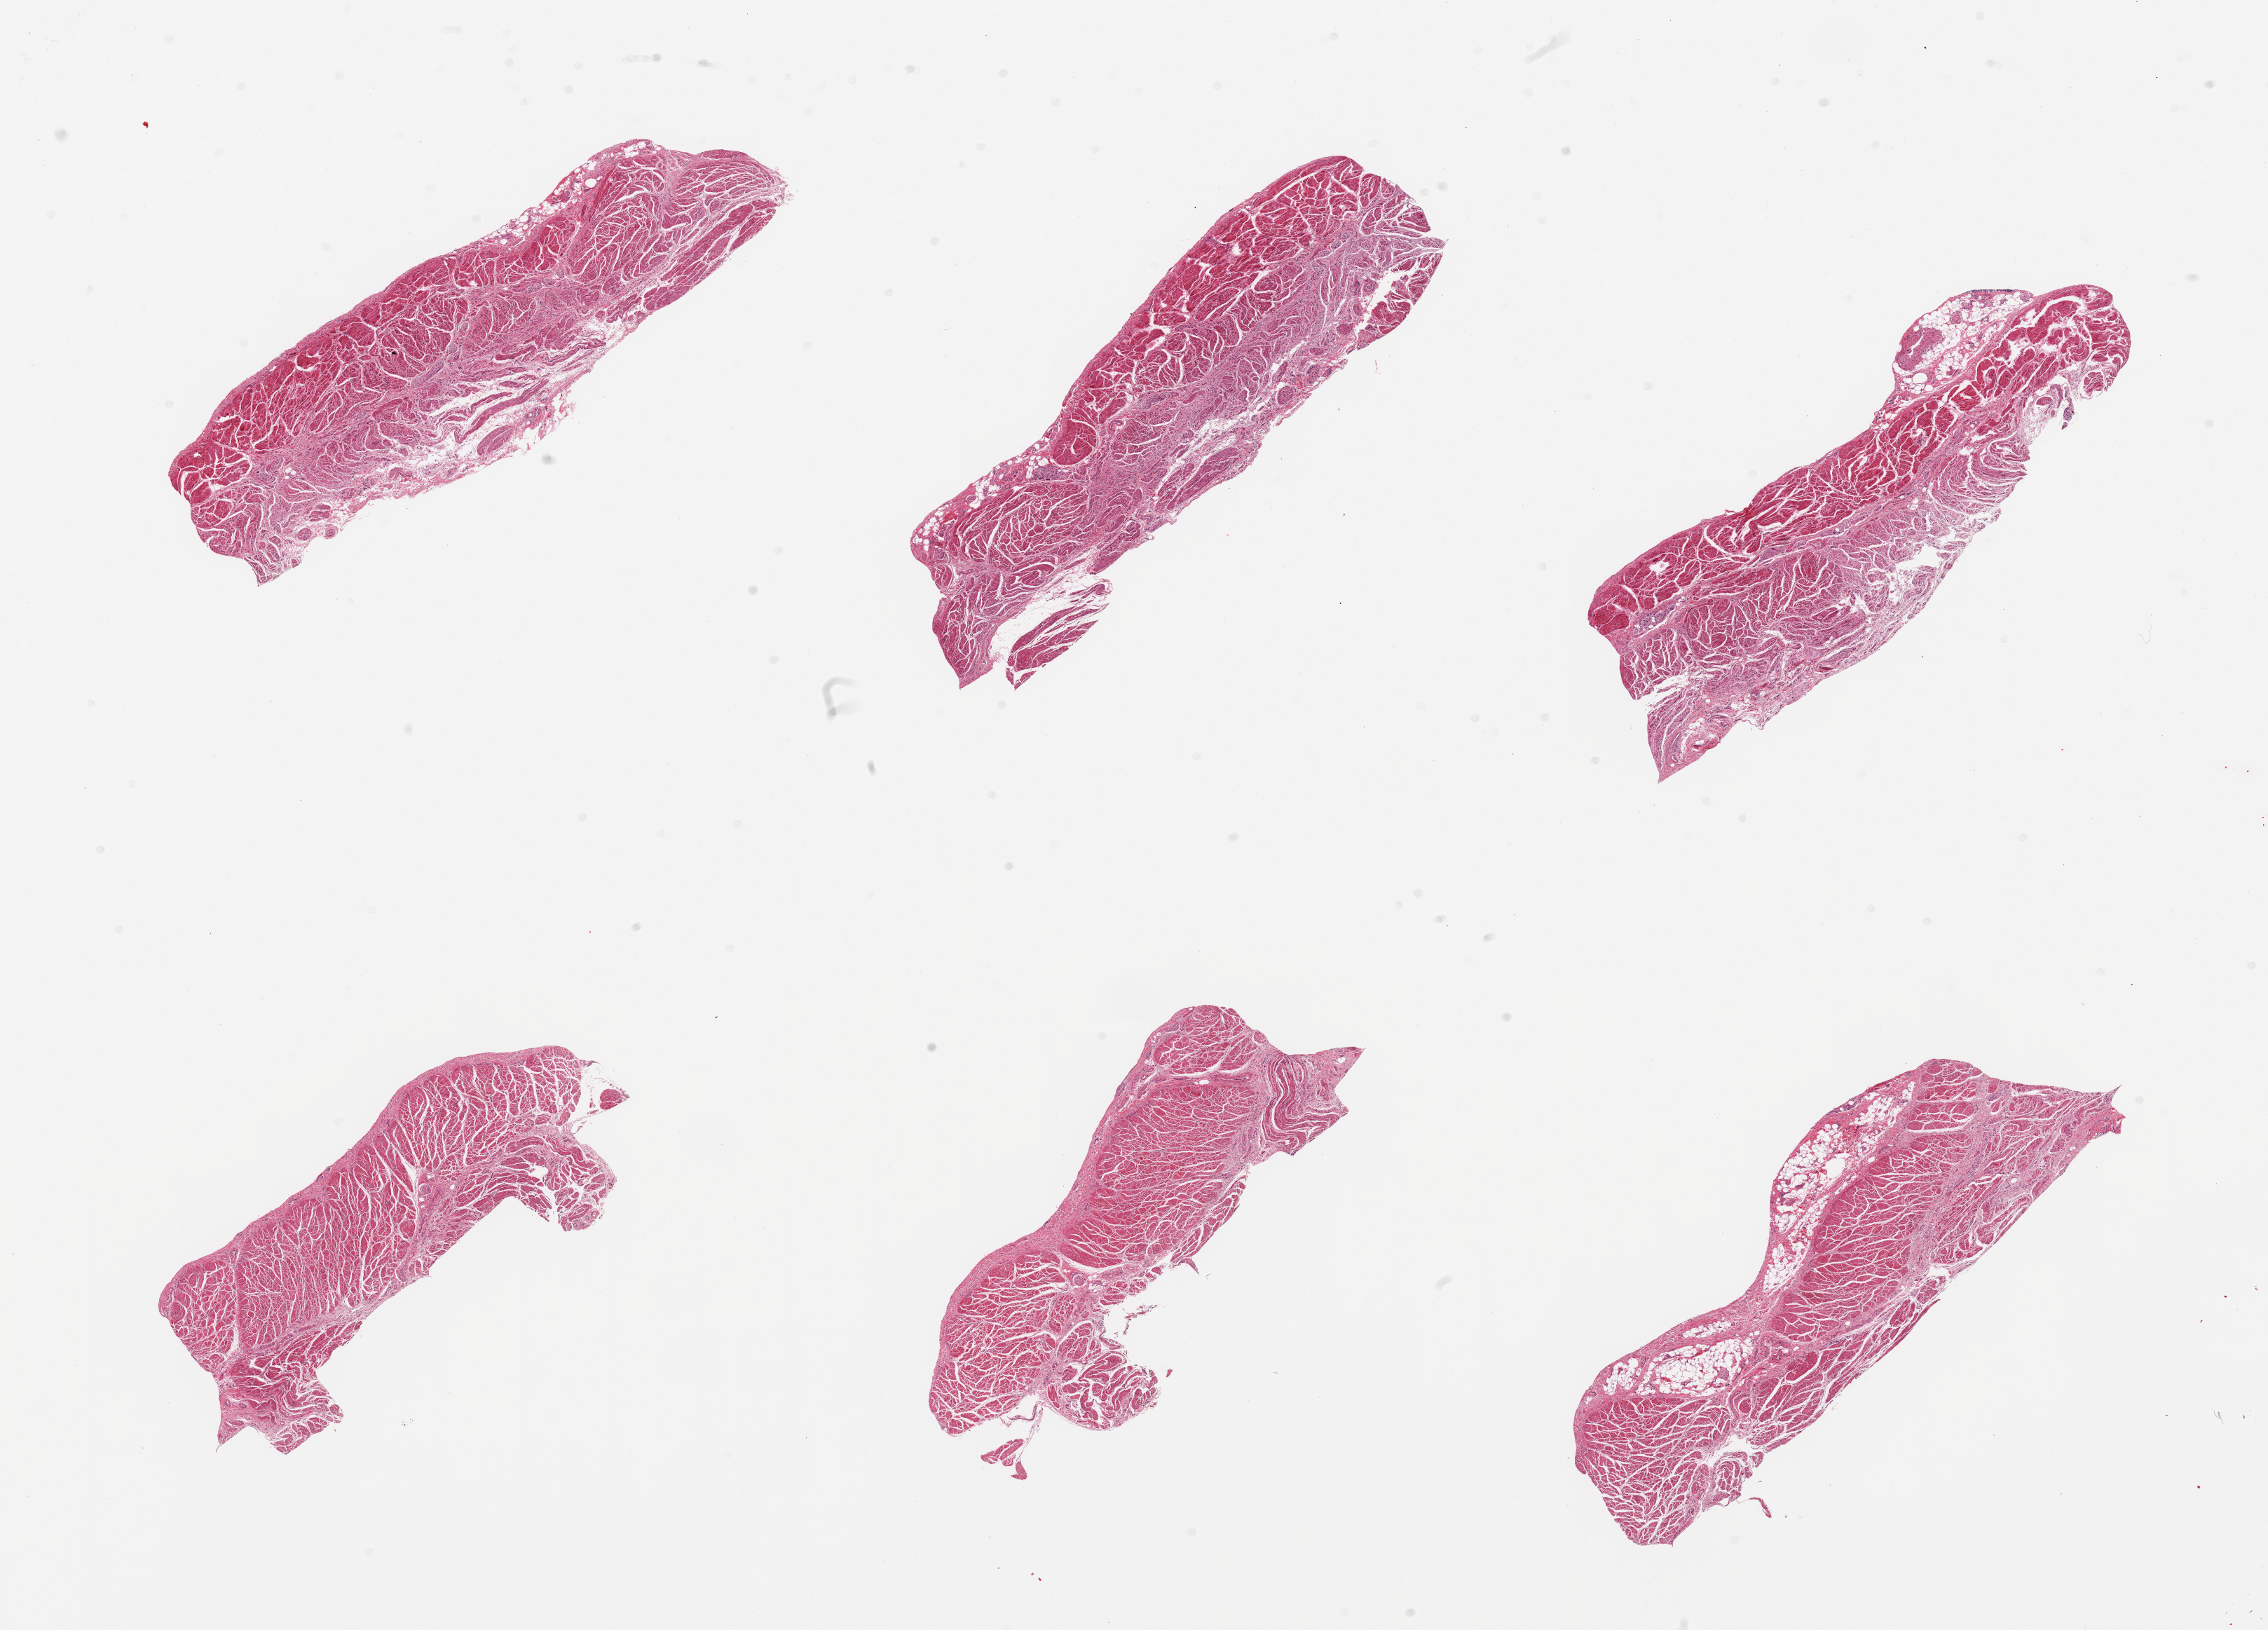
Whole-slide image, H&E stain, shown as a low-resolution overview of the whole scanned area (about 25.6 x 18.4 mm, slide scanned at 20x), PAXgene-fixed paraffin-embedded (PFPE) section, section of gastroesophageal junction (target tissue), tissue donor sample.
• review note (as recorded): 6 pieces; 20% fat on 1 of 6 pieces